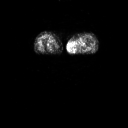
FDG PET of an extremity soft-tissue mass (from a PET/CT study), one axial slice; position 6 of 91 along the scan axis; 3.27 mm slice thickness; 128 × 128 image matrix. Patient: female, 74 years. From the clinical record (not read from this slice): histological type: pleomorphic leiomyosarcoma; grade: high; site of the primary tumour: left thigh.
Annotated regions visible in this slice (expert contour drawn on MRI and transferred to this co-registered scan by the dataset authors):
- gross tumour volume including surrounding oedema: box from (x=72, y=37) to (x=87, y=50) px